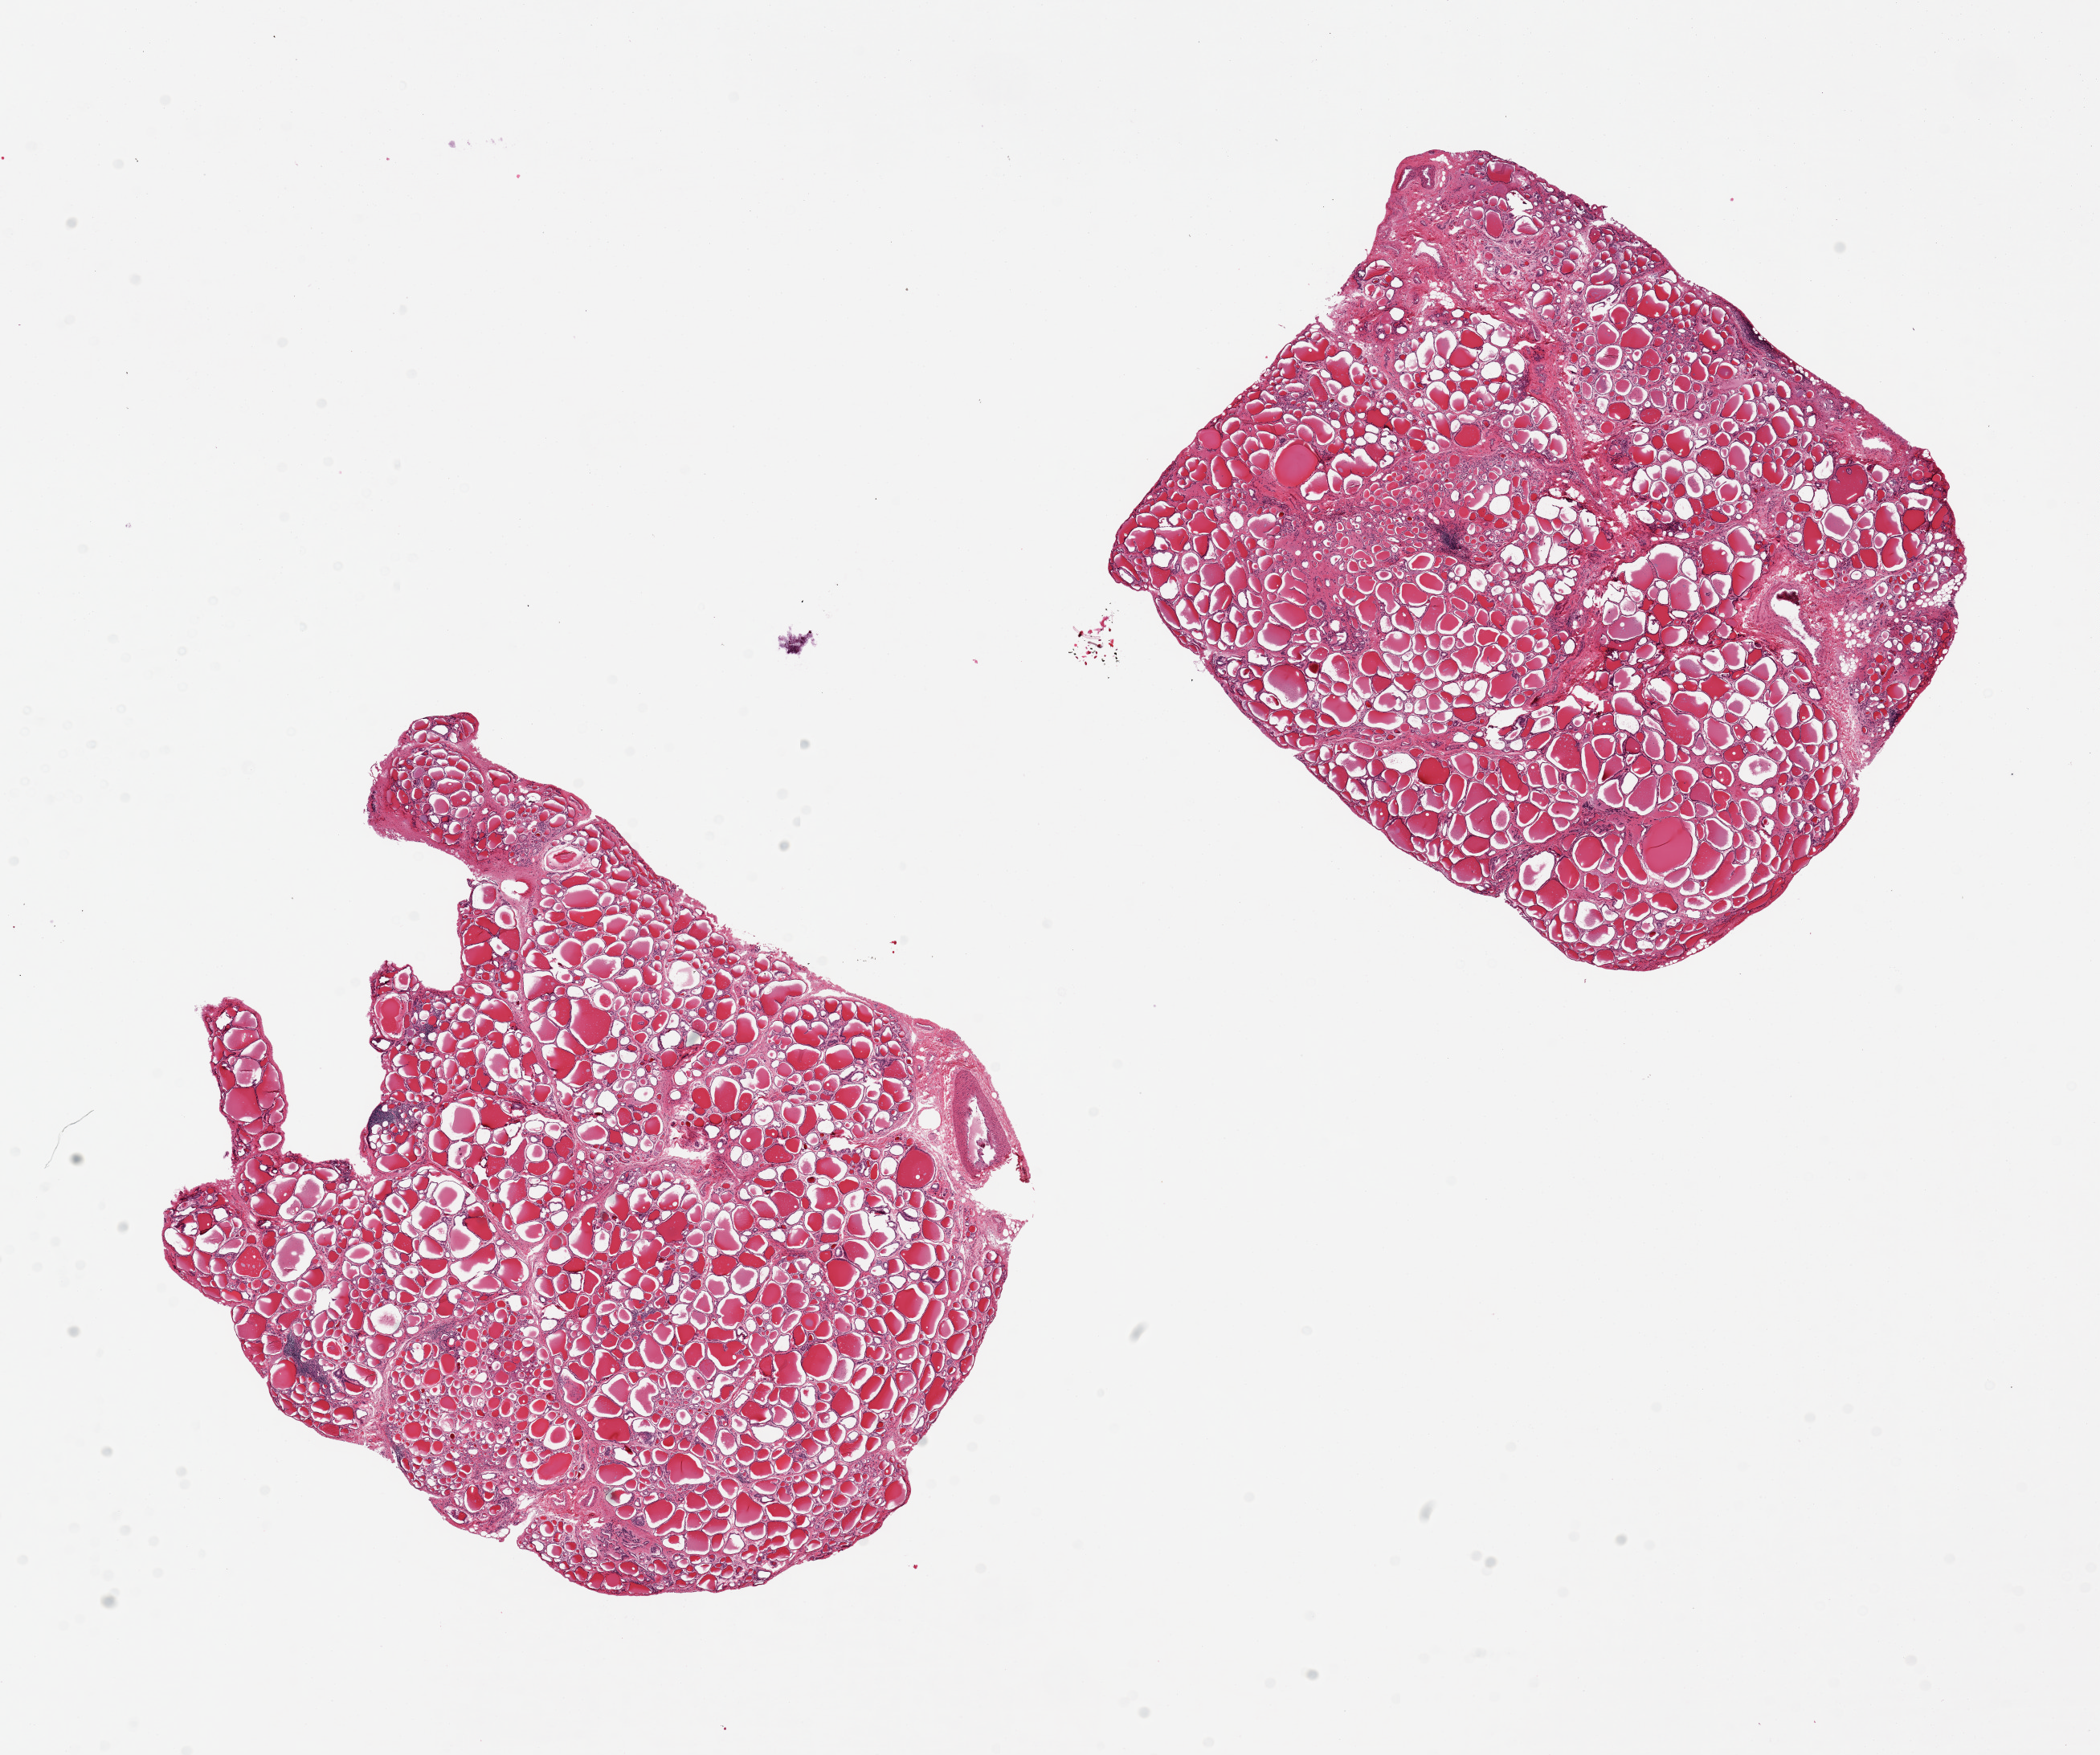
Digitized H&E-stained section — whole scanned area (about 20.7 x 17.3 mm) shown as a low-resolution overview; PAXgene-fixed paraffin-embedded (PFPE) section; target tissue: thyroid; donor tissue sample. Male donor.
Reviewer comment on this tissue sample: 2 pieces, 8x7 & 7.5x6mm; a few small focal lymphoid collections.